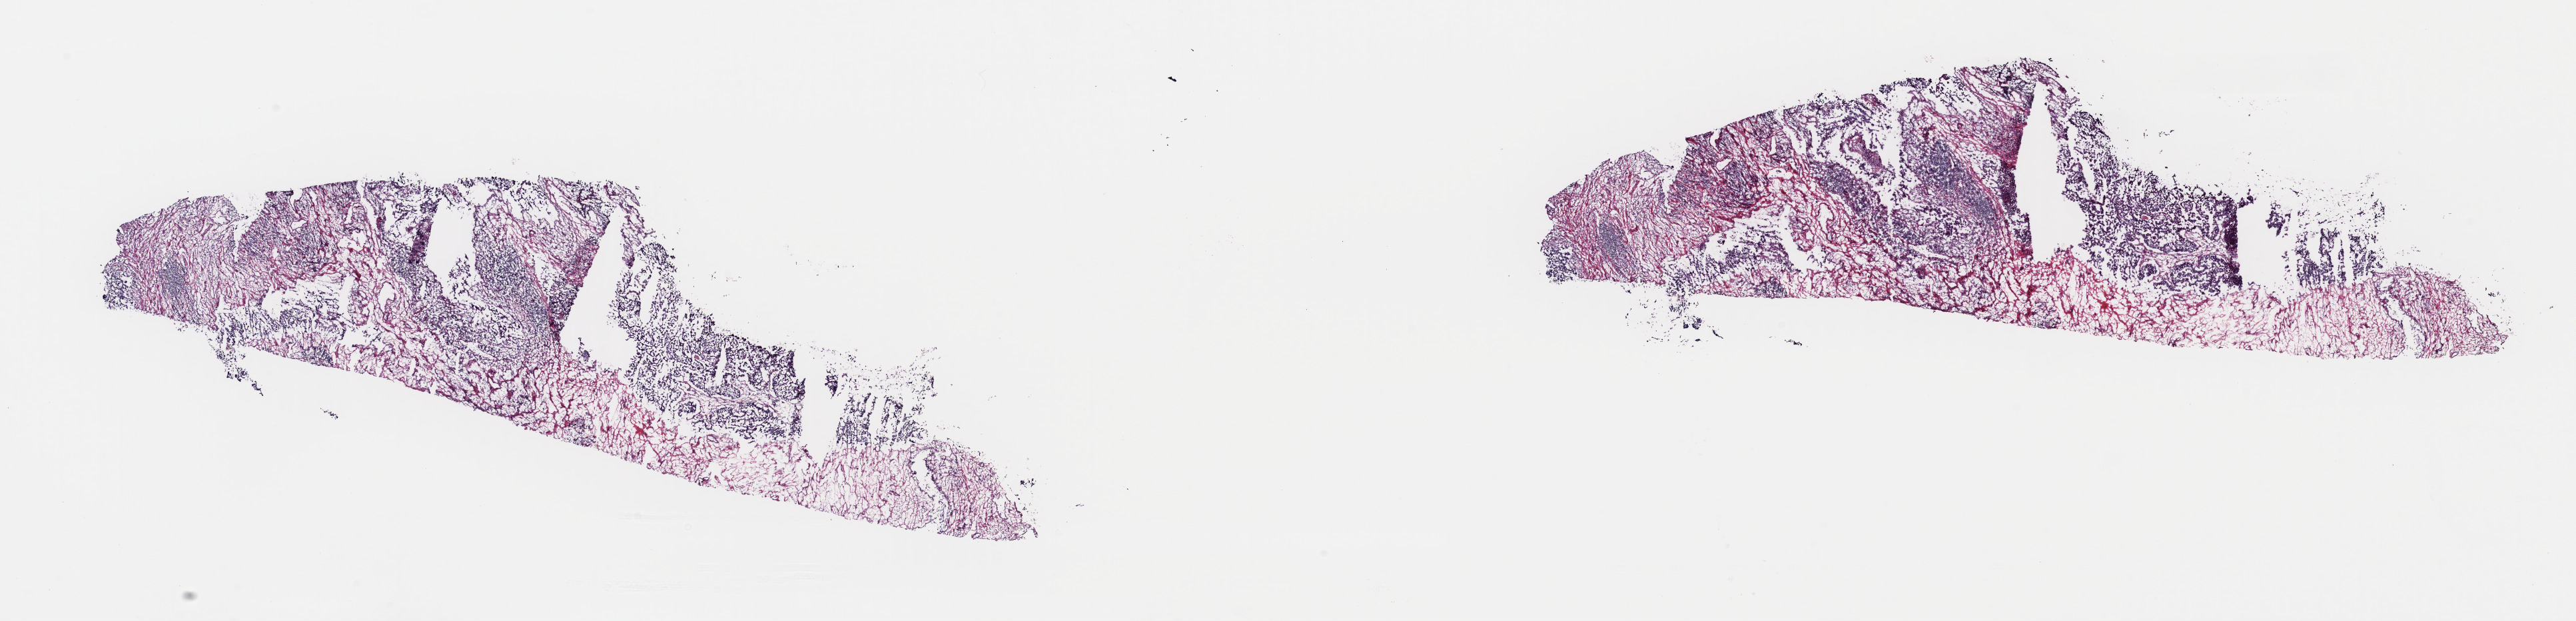
Whole-slide histology image, H&E — low-resolution overview of the scanned area, about 30.5 x 7.4 mm. Frozen section from the top of the tissue portion. Bladder, primary tumour sample. Male patient; age at initial diagnosis 71 years. Histologic grade: high grade. Pathologist review of this section (percent, as recorded): tumour cells 70%, tumour nuclei 70%, normal cells 0%, stromal cells 30%, necrosis 0%. Infiltration values recorded for this section: lymphocyte infiltration 8%, monocyte infiltration 0%, neutrophil infiltration 0%.
Lymph nodes positive (case pathology): 0 of 7 examined. AJCC pathologic stage: II (6th edition). Histologic diagnosis: Transitional cell carcinoma (lateral wall of bladder).